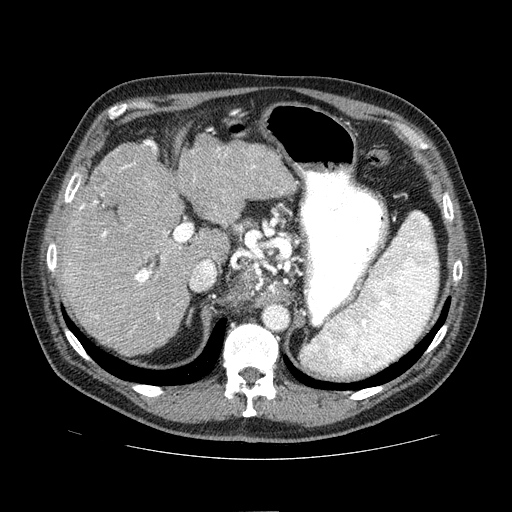
Contrast-enhanced abdominal CT (liver protocol), one axial slice; position 48 of 81 along the scan axis; 100 kVp; one of 2 acquisitions stored at this slice position; soft-tissue window (W 400 / L 40 HU); 2.5 mm slice thickness; 512 × 512 image matrix, field of view 400 × 400 mm. From the clinical record (not read from this slice): diagnosis: hepatocellular carcinoma (patient treated with transarterial chemoembolisation; whether this scan precedes or follows treatment is not stated here); TNM stage (as recorded): Stage-IIIA; Child-Pugh class: A.
Outlined on this slice (semi-automatically segmented with operator editing):
- liver parenchyma outside the tumour (the mass and vessels are separate outlines, so this box may not span the whole liver): box from (x=58, y=131) to (x=296, y=354) px
- liver vessels: (x=80, y=140)–(x=256, y=328)